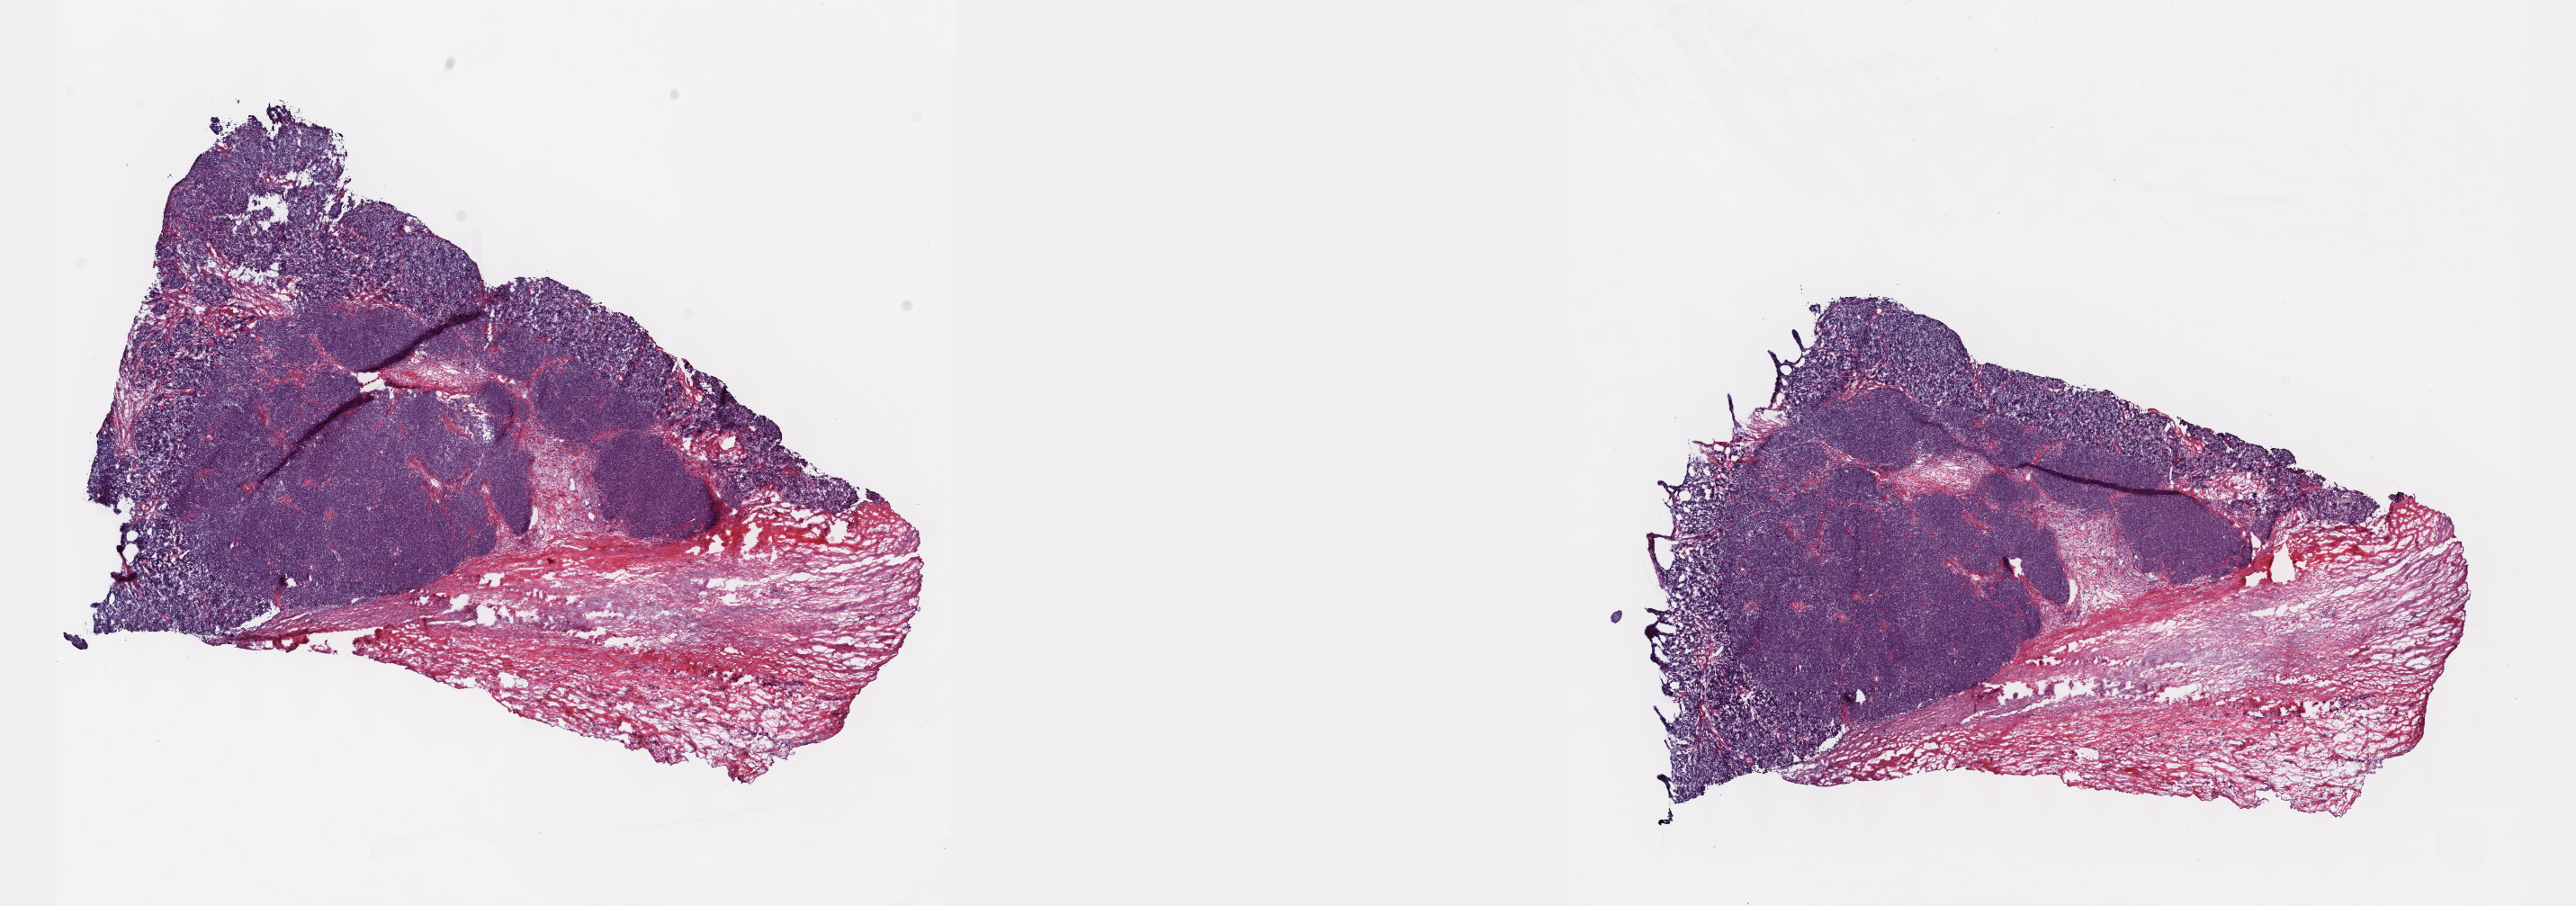
Digitized H&E tissue section (whole slide), whole scanned area (about 23.1 x 8.1 mm, slide scanned at 40x) shown as a low-resolution overview. Frozen section from the top of the tissue portion. Thymus, primary tumour sample. Male, age 53 years at initial diagnosis. Composition of this section per pathologist review: tumour cells 70%, tumour nuclei 90%, normal cells 0%, stromal cells 30%, necrosis 0%. Infiltration values recorded for this section: lymphocyte infiltration 0%, monocyte infiltration 0%, neutrophil infiltration 0%.
Pathologic diagnosis: Thymoma, type AB, malignant.